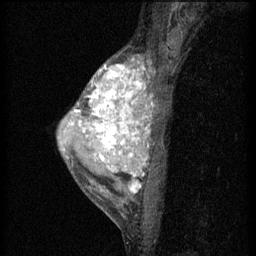
Breast MRI (dynamic contrast-enhanced), one sagittal slice; position 38 of 60 along the scan axis; 3 images stored at this slice position (order not interpretable as contrast timing); 1.5 T; TE 4.2 ms, TR 11 ms; 256 × 256 image matrix, field of view 180 × 180 mm. Female patient, age 40 years.
Structures marked on this image (semi-automatic segmentation, software-assisted and operator-edited):
- analysis volume of interest (the breast-tissue region the enhancement analysis was run in; not a lesion): bounding box (x1, y1, x2, y2) in pixels: (58, 54, 159, 203)
- tumour enhancement mask (voxels above the 70 % enhancement threshold inside the analysis volume of interest): (75, 62, 154, 193)